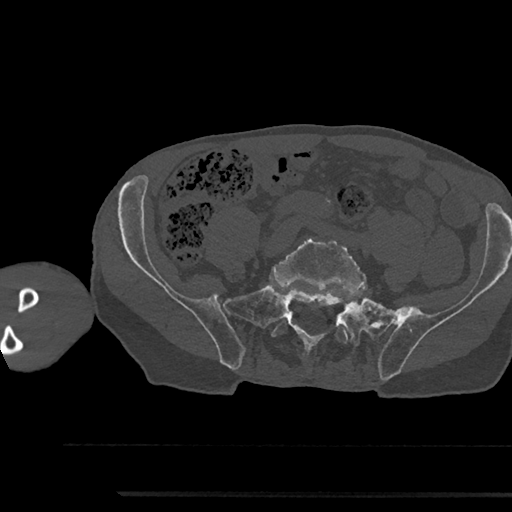
CT including the spine, one axial slice; slice 316 of 797 in the series (ordered by position); reconstruction kernel Br40s/3; 120 kVp; bone window (W 1800 / L 400 HU); 0.5 mm slice thickness; 512 × 512 image matrix, field of view 367 × 367 mm. Male patient, age 79 years. From the clinical record (not read from this slice): primary cancer: prostate.
Annotated regions visible in this slice (semi-automatic segmentation, software-assisted and operator-edited):
- L5 vertebra: box from (x=271, y=235) to (x=367, y=343) px